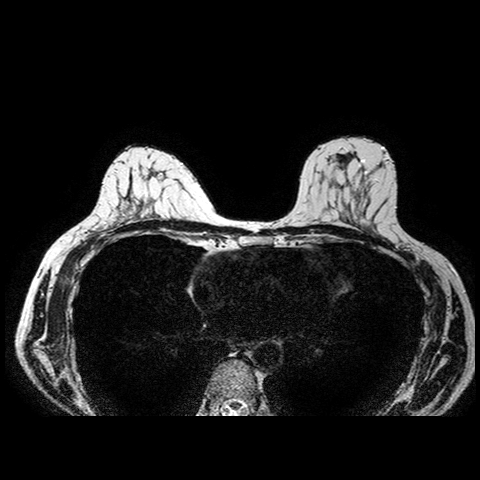
Breast MRI examination; 2 images, each one mid-volume slice chosen by position. Patient in her 50s.
Image 1: axial T2-weighted / STIR image, slice 43 of 84.
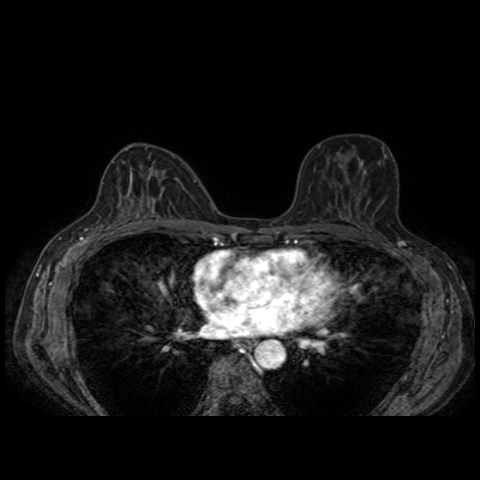
Image 2: axial dynamic contrast-enhanced T1-weighted image, slice 43 of 84, dynamic phase 5 of 8, 4 mm slice thickness.
Radiologist's MRI impression: LEFT BREAST: There is minimal background enhancement. In the left upper outer breast very superficial there is a biopsy clip seen approx 1-2 o'clock mid-depth. Surrounding the susceptibility artefact of the clip, there no remnant mass or suspicious enhancement seen. Exactly 1.5 cm inferior and 1.0 cm medial to the clip there is a linear area of indeterminate enhancement seen measuring 0.7 x 0.4 cm; this might be vascular, however it is recommended to include this area in the surgical plan. Otherwise no suspicious enhancement, masses, or areas of architectural distortion seen within the left breast. There is no skin thickening, nipple inversion, or left axillary lymphadenopathy present. RIGHT BREAST: There is minimal background enhancement. No foci of suspicious enhancement, masses, or areas of architectural distortion seen within the right breast. There is no skin thickening, nipple inversion, or right axillary lymphadenopathy present. IMPRESSION: 1) No remnant mass seen in the area of the artifact caused by the biopsy clip, marking the area of the known cancer in the upper outer very superficial breast, mid depth, at approx. 1-2 o'clock. 2) Exactly 1.5 cm inferior and 1 cm medial to the biopsy clip there is an linear area of indeterminate enhancement seen, measuring 7 x 4 mm, which is possibly vascular, however should be included in the surgical plan, to rule out DCIS. Otherwise, no additional suspicious area in the left breast. No left lymphadenopathy. 3) Unremarkable right breast and axilla. No evidence of malignancy of the contralateral right breast. No right axillary lymphadenopathy ; BI-RADS 6.
Pathology recorded for this patient (not read from these images): pathology diagnosis: Invasive Lobular Carcinoma (left breast); pathology report notes: Invasive Lobular Carcinoma. Size of Invasive component: 0.6x0.5cm; clinical background (as recorded): 50s y.o. with recent diagnosed left breast CA.